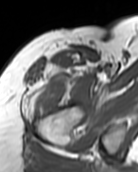
MRI of an extremity soft-tissue mass, one axial slice. Position 85 of 99 along the scan axis. MR volume resampled by the dataset authors to the PET/CT grid (not the native acquisition matrix). 3.27 mm slice thickness. 138 × 172 image matrix. Female patient. Case-level facts recorded for this patient, not image findings: histological type: pleiomorphic undifferentiated sarcoma; grade: high; site of the primary tumour: right quadricep.
Outlined on this slice (expert contour drawn on MRI and transferred to this co-registered scan by the dataset authors):
- gross tumour volume including surrounding oedema: bounding box [x1, y1, x2, y2] px = [34, 80, 61, 117]